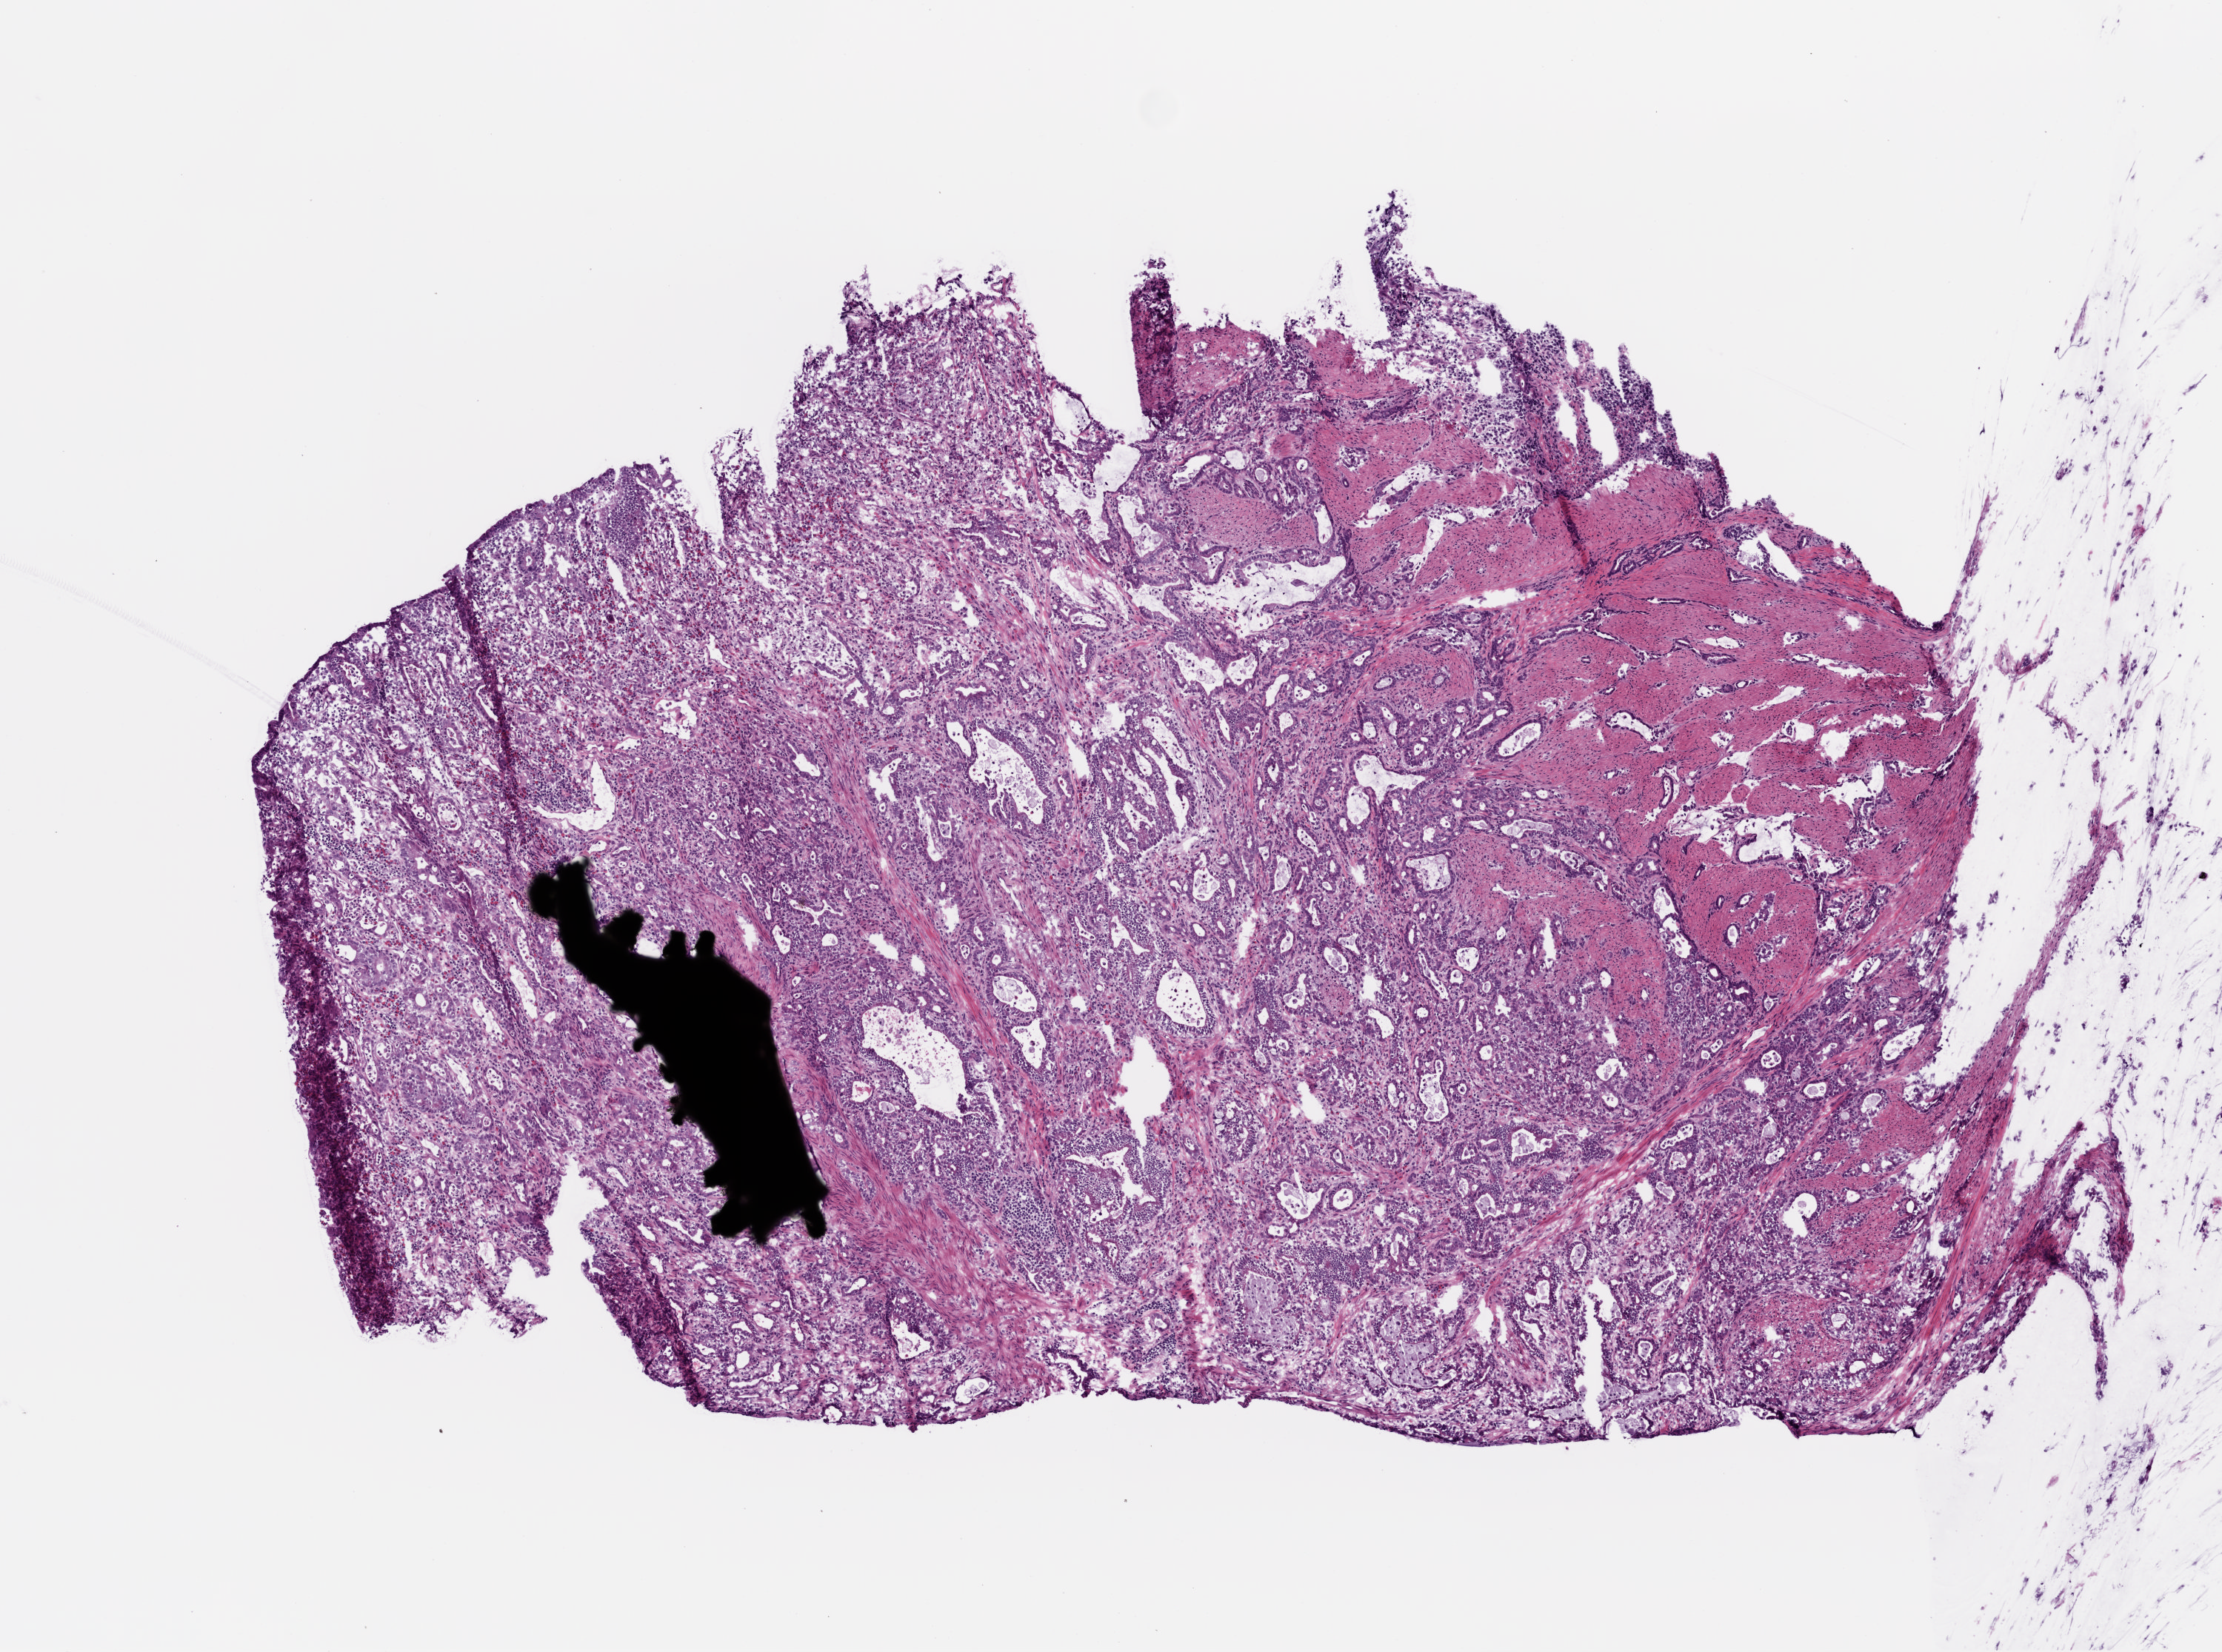
H&E-stained whole-slide image, whole scanned area (about 6.0 x 4.5 mm) shown as a low-resolution overview; frozen section from the bottom of the tissue portion; stomach, primary tumour sample. Female, age 54 years at initial diagnosis. Histologic grade: G1 (well differentiated). Pathologist review of this section (percent, as recorded): tumour cells 85%, tumour nuclei 70%, normal cells 0%, stromal cells 15%, necrosis 0%.
• lymph nodes positive (case pathology): 0 of 15 examined
• pathologic diagnosis: Adenocarcinoma, intestinal type (body of stomach)
• AJCC pathologic stage: IV